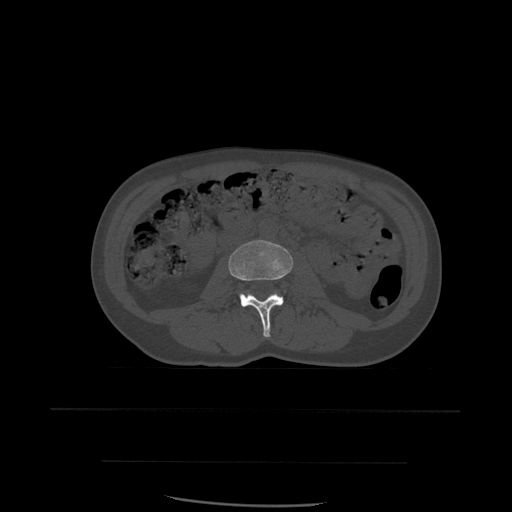
CT including the spine, one axial slice; position 194 of 574 along the scan axis; bone window (W 1800 / L 400 HU); 1.25 mm slice thickness; 512 × 512 image matrix, field of view 392 × 392 mm. Patient age 48 years. Case-level facts recorded for this patient, not image findings: primary cancer: lung.
Outlined on this slice (semi-automatic segmentation, software-assisted and operator-edited):
- L3 vertebra: bounding box [x1, y1, x2, y2] px = [229, 240, 293, 338]